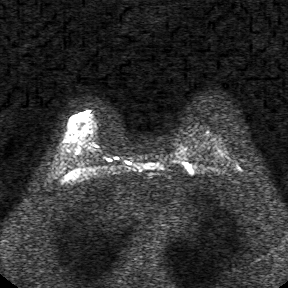
Breast MRI, one axial slice; slice 25 of 34 in the series (ordered by position); diffusion-weighted series; image 2 of 4 stored at this slice position (different b-values; order by instance number); 1.5 T; 288 × 288 image matrix, field of view 340 × 340 mm. Female patient.
Structures marked on this image (manually delineated by an expert):
- tumour on diffusion-weighted imaging: bounding box <76,111,89,117> (left, top, right, bottom; pixels)